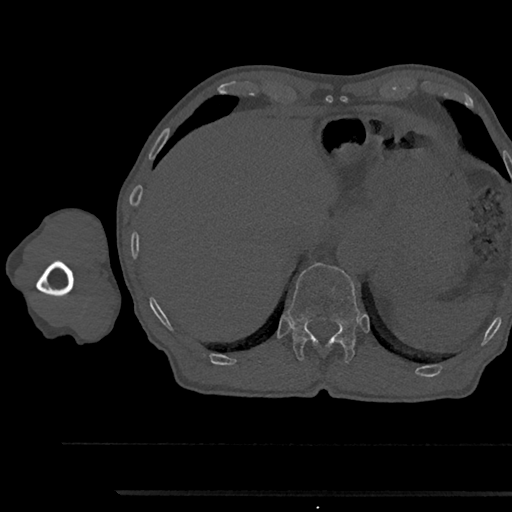
CT including the spine, one axial slice; position 734 of 797 along the scan axis; reconstruction kernel Br40s/3; 120 kVp; bone window (W 1800 / L 400 HU); 0.5 mm slice thickness; 512 × 512 image matrix, field of view 367 × 367 mm. Patient: male, 79 years. Case-level facts recorded for this patient, not image findings: primary cancer: prostate.
Annotated regions visible in this slice (semi-automatically segmented with operator editing):
- T12 vertebra: bounding box (x1, y1, x2, y2) in pixels: (287, 263, 359, 363)